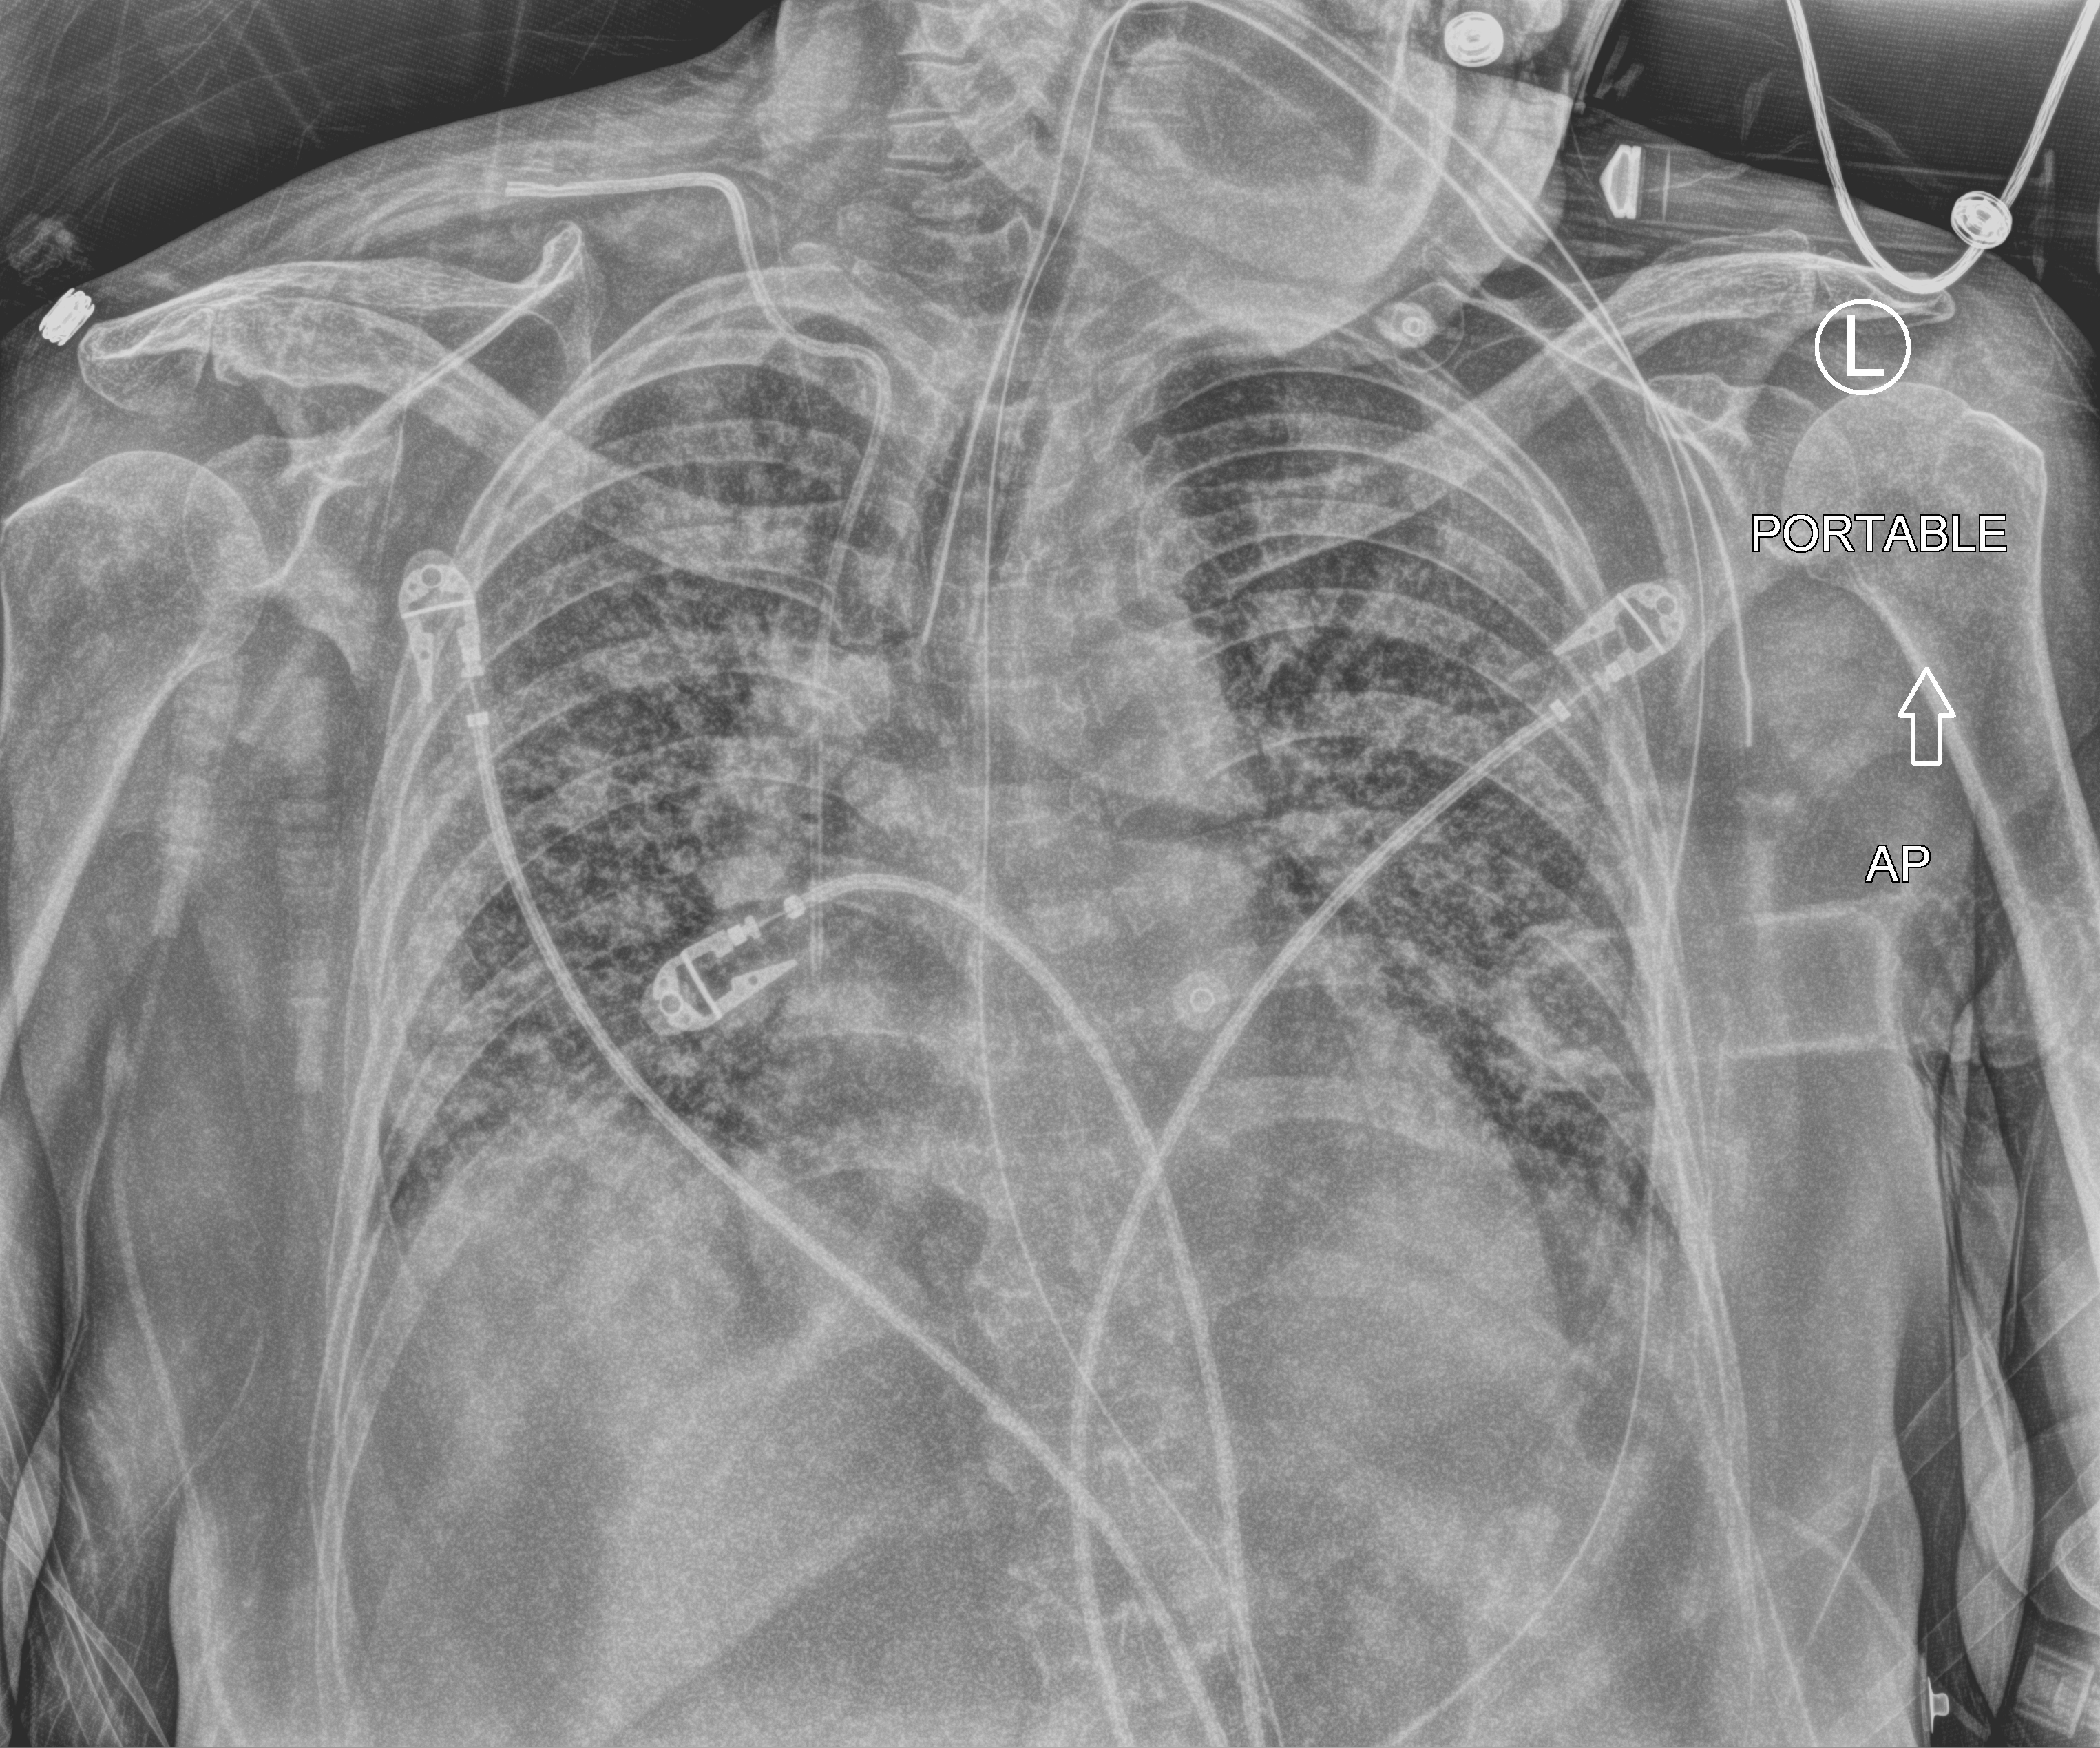
Portable chest radiograph, anteroposterior (AP) projection. Female patient hospitalised with COVID-19, age 60–74 years.
Hospital-stay facts (about this admission, not read from this image; timing relative to this image not recorded): hypertension (admission record): no; COPD (admission record): no; admitted to intensive care during this hospital stay: yes.